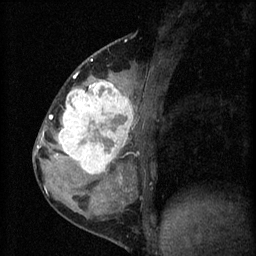
Breast MRI (dynamic contrast-enhanced), one sagittal slice; slice 25 of 60 in the series (ordered by position); 3 images stored at this slice position (order not interpretable as contrast timing); 1.5 T; TE 4.2 ms, TR 8.2 ms; 2 mm slice thickness; 256 × 256 image matrix. Patient: female, 37 years.
Outlined on this slice (semi-automatic segmentation, software-assisted and operator-edited):
- analysis volume of interest (the breast-tissue region the enhancement analysis was run in; not a lesion): bounding box (x1, y1, x2, y2) in pixels: (53, 78, 140, 181)
- tumour enhancement mask (voxels above the 70 % enhancement threshold inside the analysis volume of interest): (57, 78, 134, 179)